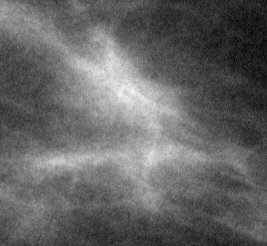
Cropped region of a digitized screen-film mammogram centred on a radiologist-marked abnormality; right breast; MLO view; BI-RADS breast density category 1 (scale 1–4).
Marked abnormality: mass, shape irregular, margins spiculated; BI-RADS assessment category 5; subtlety rating 4 on a 1 (subtle) to 5 (obvious) scale; pathology (as recorded): malignant.